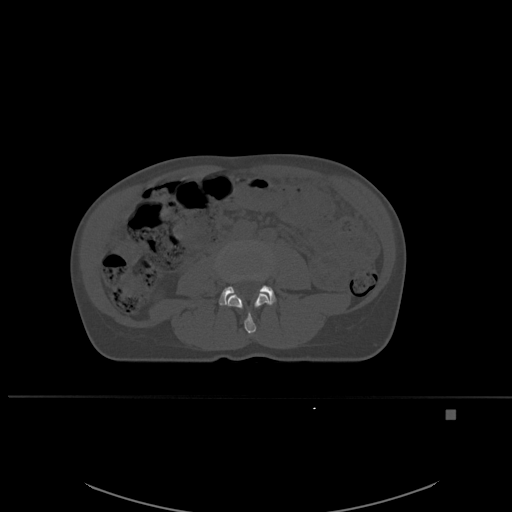
CT including the spine, one axial slice; position 203 of 537 along the scan axis; bone window (W 1800 / L 400 HU); 512 × 512 image matrix, field of view 440 × 440 mm. Patient: female, 45 years. From the clinical record (not read from this slice): primary cancer: lung.
Outlined on this slice (semi-automatically segmented with operator editing):
- L3 vertebra: box from (x=227, y=292) to (x=271, y=334) px
- L4 vertebra: (x=219, y=286)–(x=276, y=305)